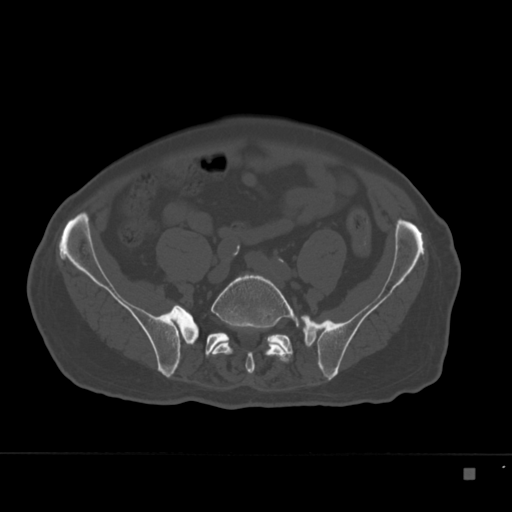
CT including the spine, one axial slice; position 17 of 332 along the scan axis; reconstruction kernel Br40s; 120 kVp; bone window (W 1800 / L 400 HU); 512 × 512 image matrix. Patient: male, 72 years. From the clinical record (not read from this slice): primary cancer: skeletal.
Outlined on this slice (semi-automatic segmentation, software-assisted and operator-edited):
- L5 vertebra: bounding box <207,274,300,374> (left, top, right, bottom; pixels)